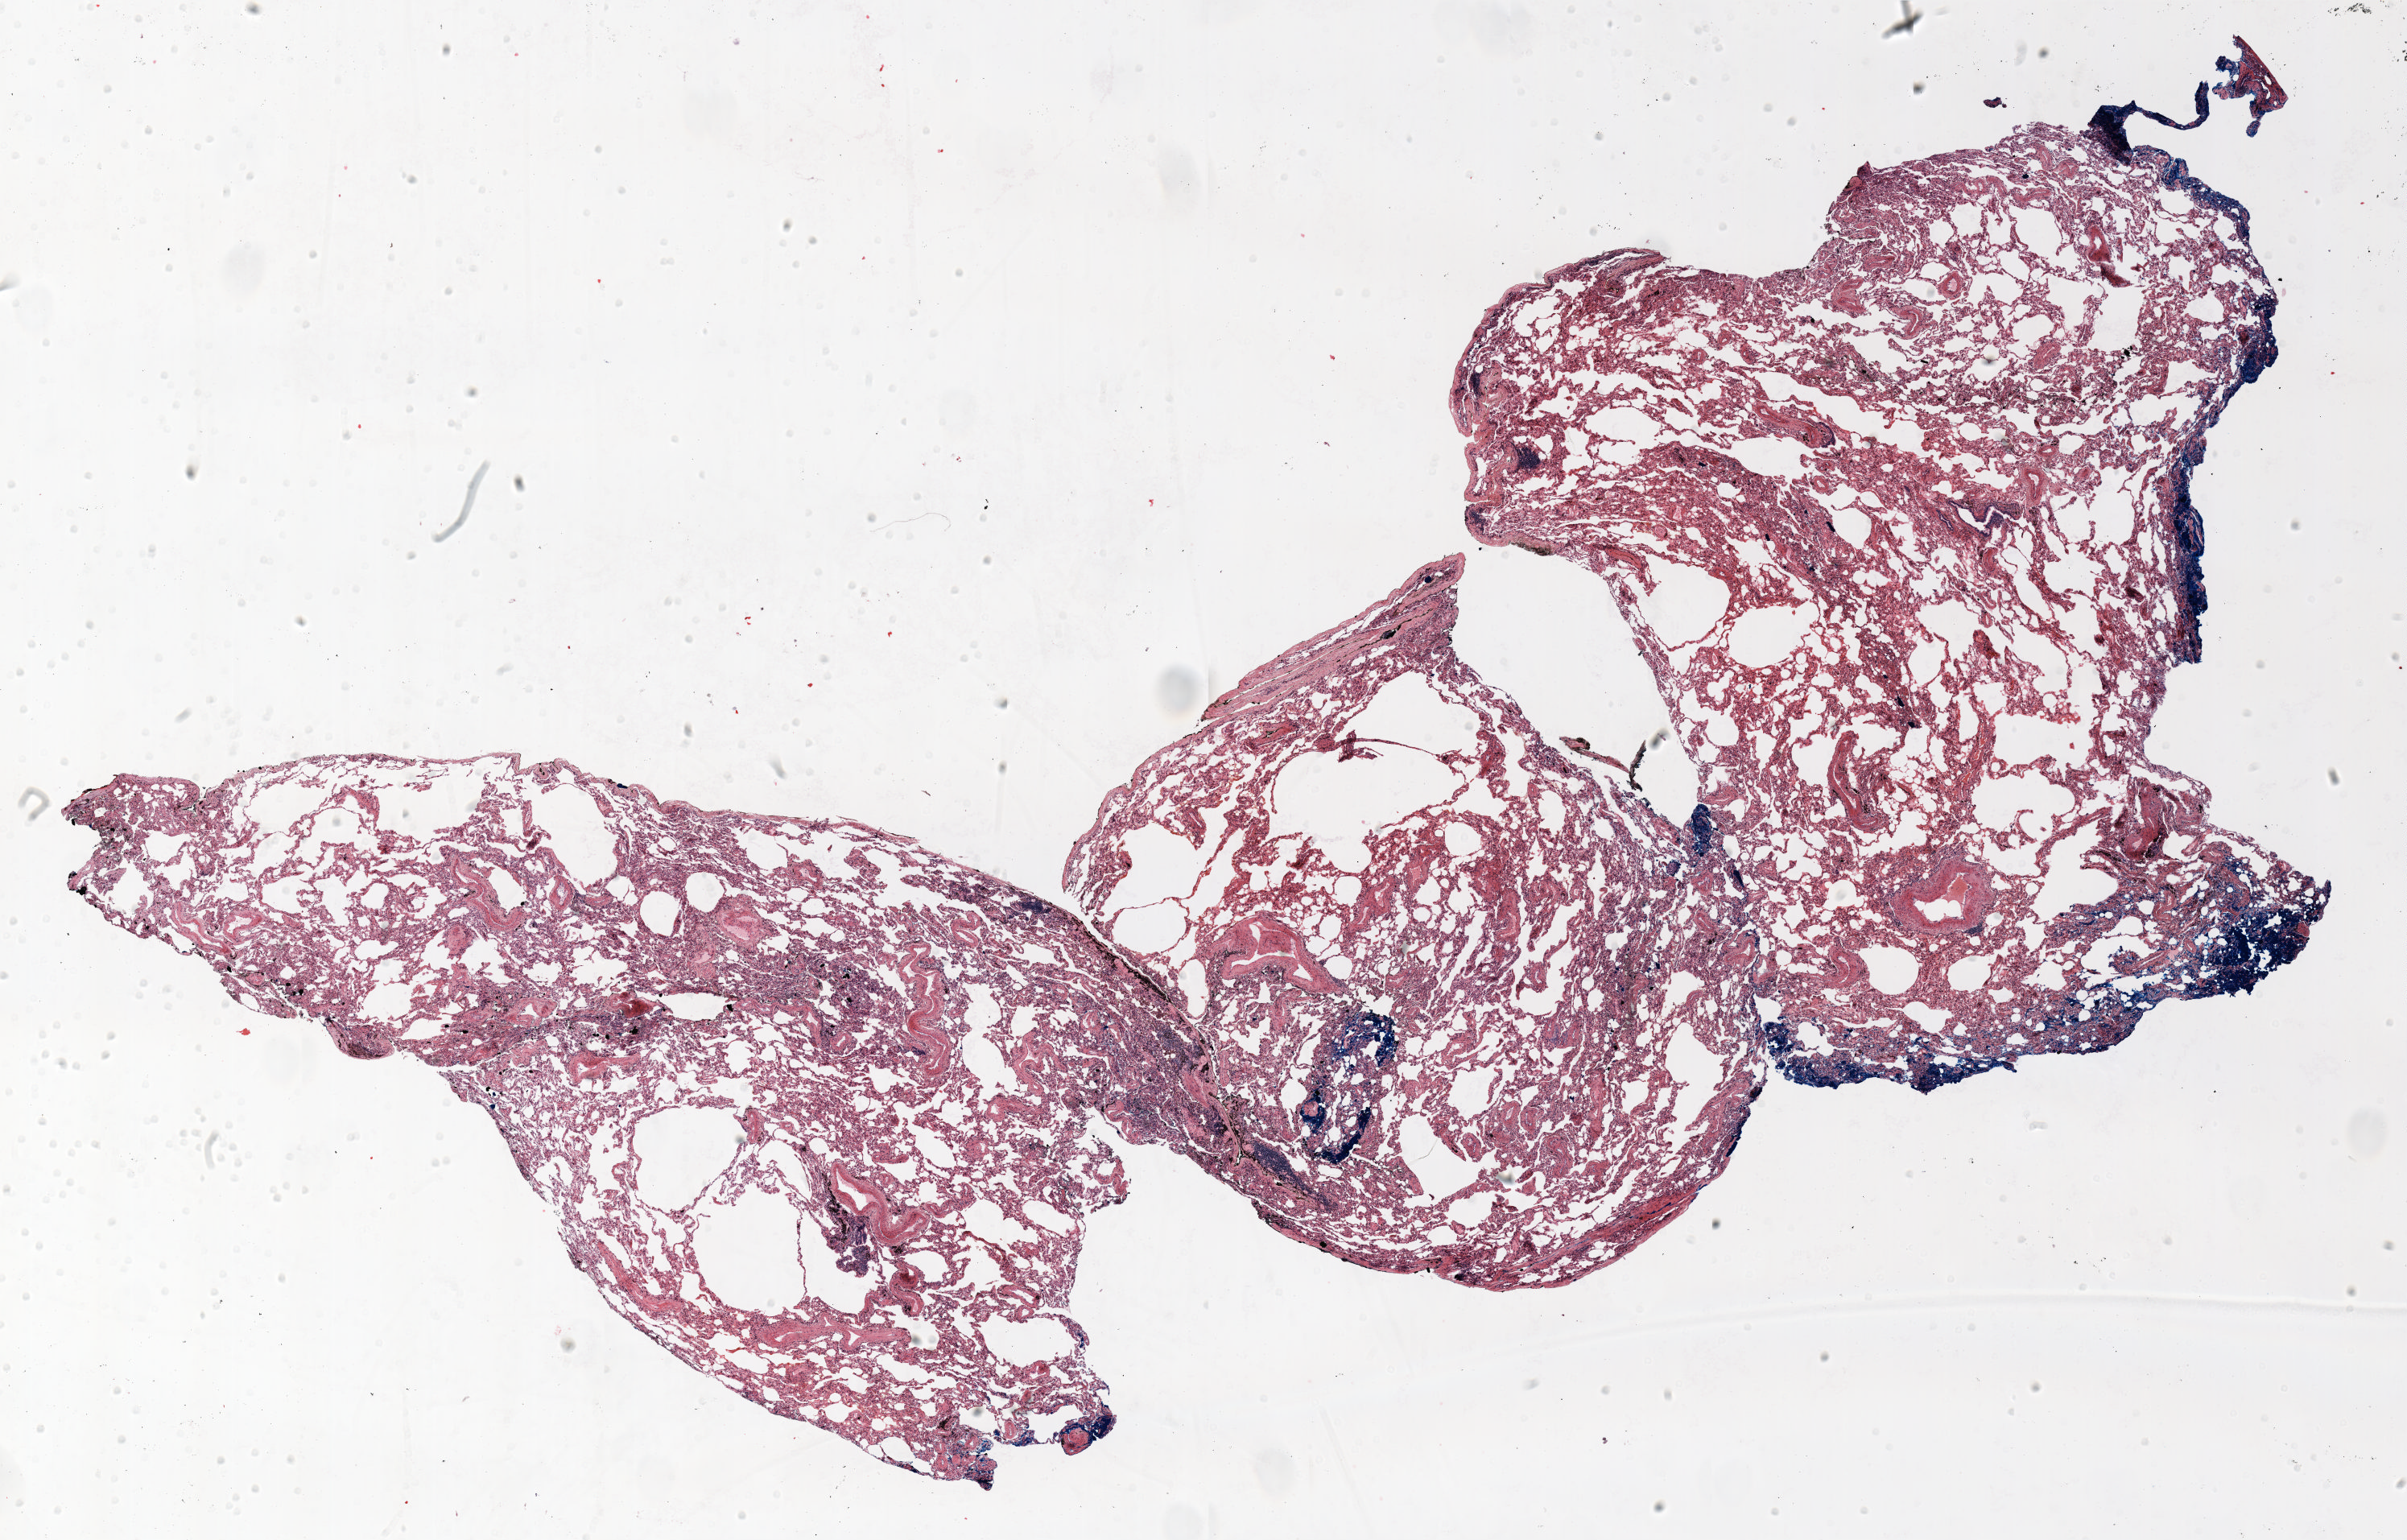
Whole-slide histology image, Hematoxylin and eosin (H&E) stained — shown as a low-resolution overview of the whole scanned area (about 24.0 x 15.4 mm, acquisition: 20x scan), FFPE section, lung. Male patient, aged 63 at enrolment. Current smoker at enrolment. Grade: poorly differentiated (G3).
- tumour size (pathology): 4 mm
- stage (AJCC 6th edition): IA
- primary tumour location (clinical record): left lower lobe
- participant's lung-cancer diagnosis: Squamous cell carcinoma, NOS
- ICD-O-3 topography: lower lobe of lung (C34.3)